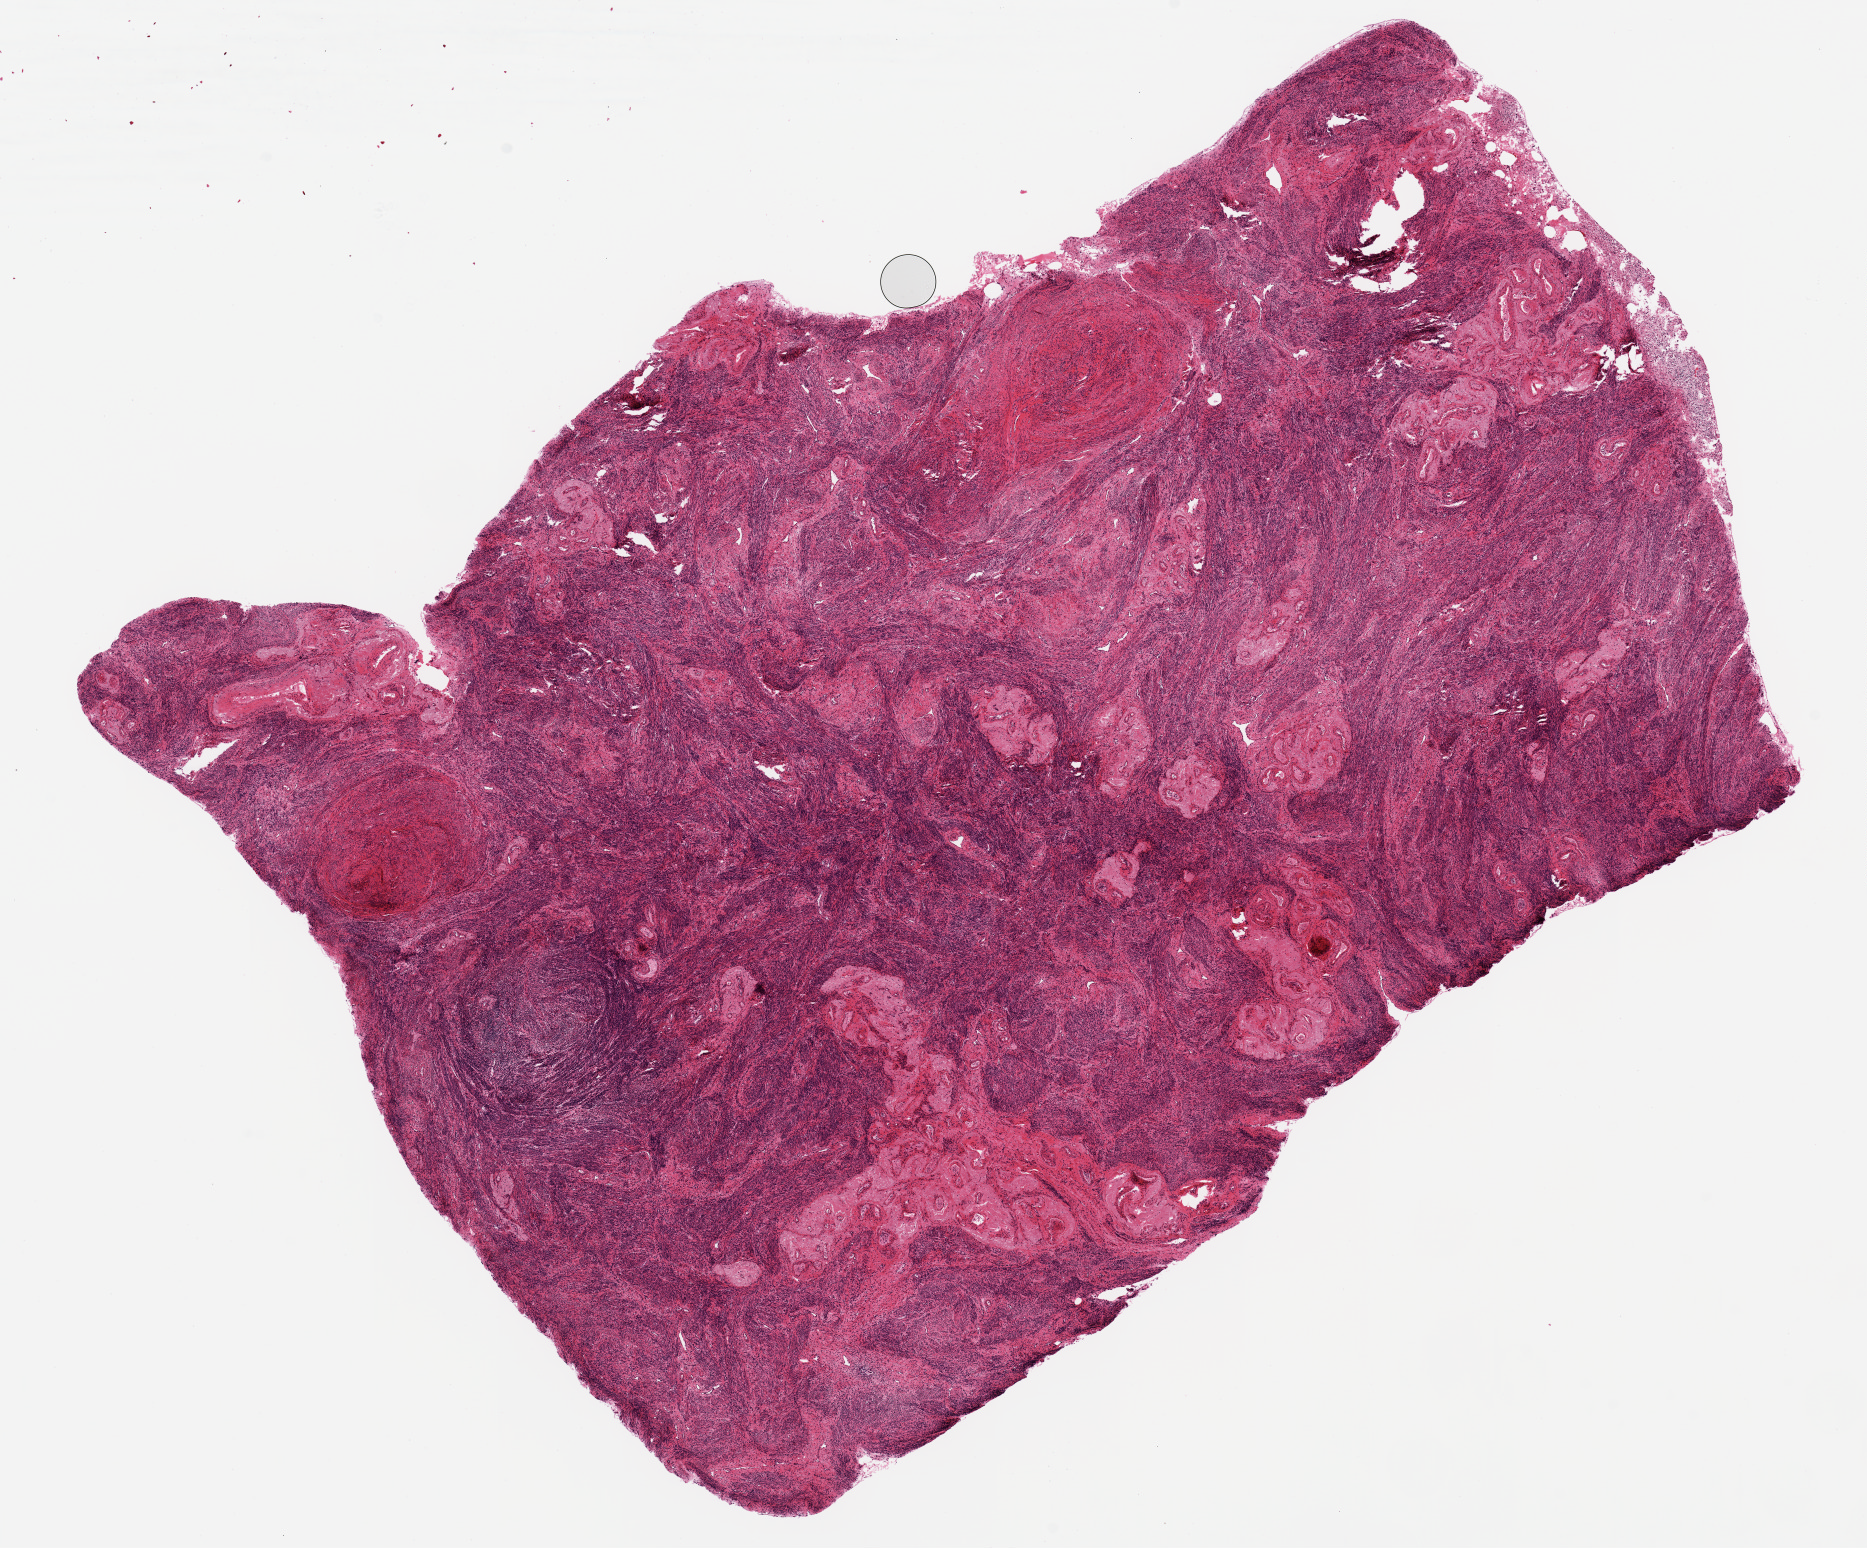
Haematoxylin and eosin whole-slide image — shown as a low-resolution overview of the whole scanned area (about 14.8 x 12.2 mm), PAXgene-fixed paraffin-embedded (PFPE) section, sampled site (target tissue): uterus, donor tissue sample. Donor sex: female.
Pathologist's review note for this sample: Glands,1. Stroma. 12x8.8mm.